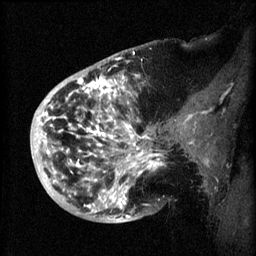
Breast MRI (dynamic contrast-enhanced), one sagittal slice; slice 19 of 60 in the series (ordered by position); 3 images stored at this slice position (order not interpretable as contrast timing); 1.5 T; TE 4.2 ms, TR 8.2 ms; 2 mm slice thickness; 256 × 256 image matrix, field of view 200 × 200 mm. Female patient, age 50 years.
Annotated regions visible in this slice (semi-automatic segmentation, software-assisted and operator-edited):
- analysis volume of interest (the breast-tissue region the enhancement analysis was run in; not a lesion): bounding box <44,72,173,219> (left, top, right, bottom; pixels)
- tumour enhancement mask (voxels above the 70 % enhancement threshold inside the analysis volume of interest): <44,76,163,219>